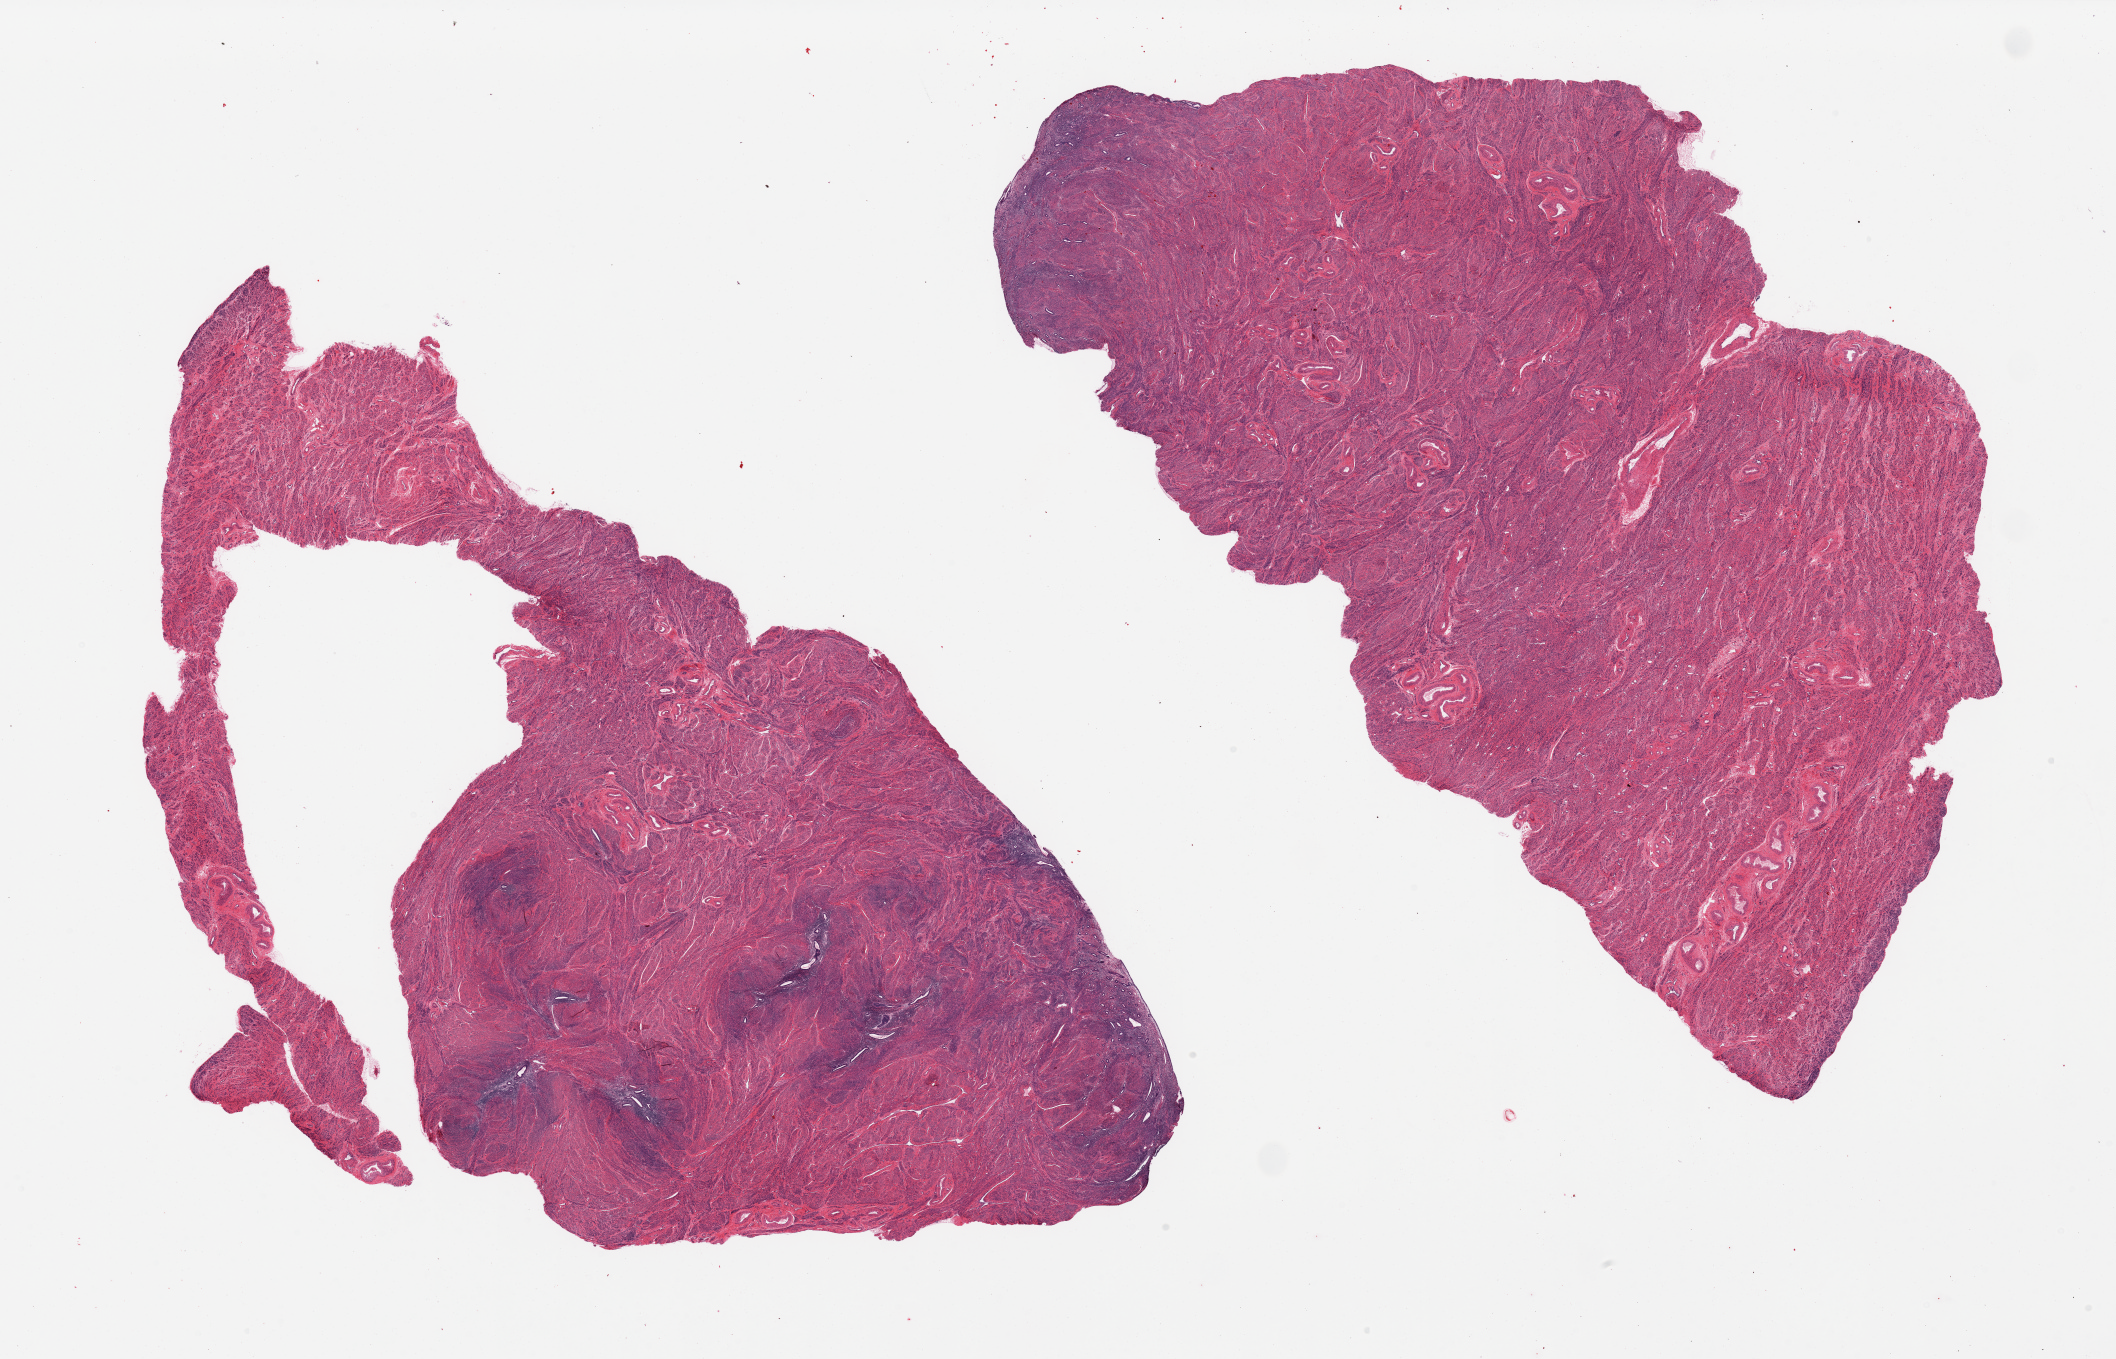
Whole-slide image, hematoxylin and eosin (H&E) stain — a low-resolution overview of the entire scanned area, about 33.5 x 21.5 mm, PAXgene-fixed paraffin-embedded (PFPE) section, sampled site (target tissue): uterus, tissue donor sample. Donor sex: female.
Pathologist's review note for this sample: 2 pieces, myometrium, foci of adenomyosis in one section.